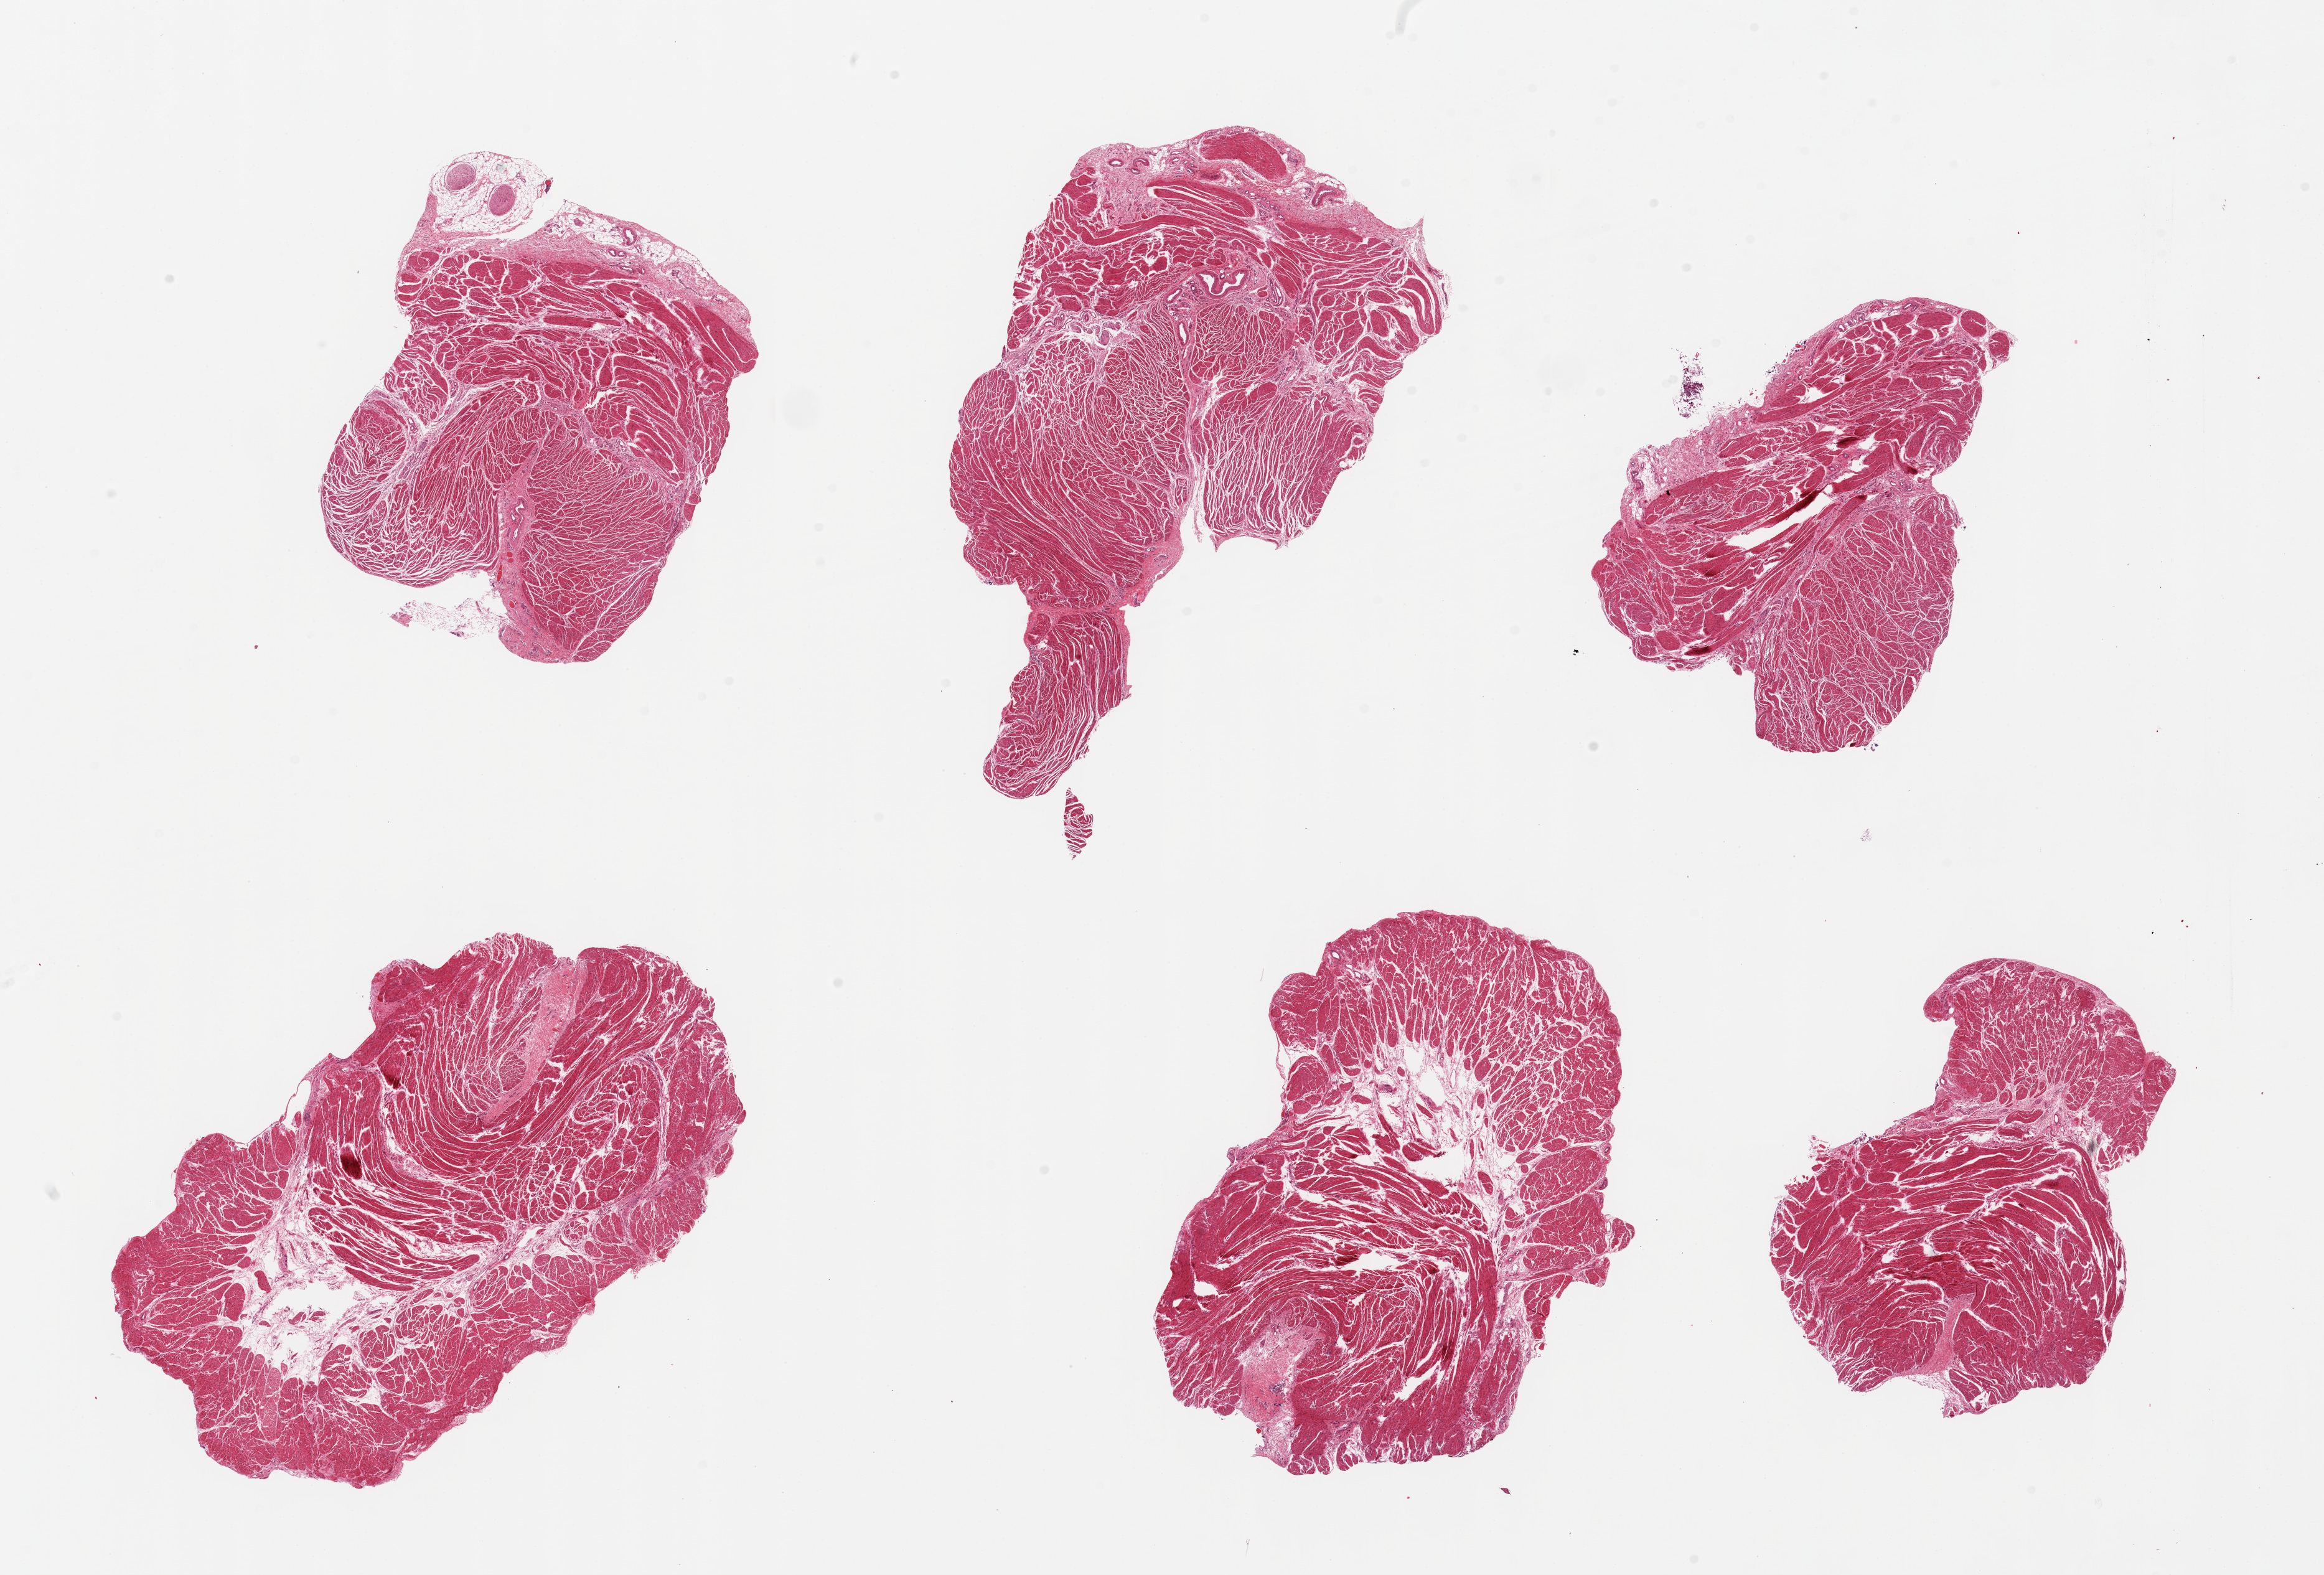
Digitized H&E-stained section, brightfield, shown as a low-resolution overview of the whole scanned area (about 29.5 x 20.0 mm, acquisition: 20x scan), PAXgene-fixed paraffin-embedded (PFPE) section, sampled site (target tissue): gastroesophageal junction, tissue donor sample. Female donor.
• reviewer comment on this tissue sample: 6 pieces; well trimmed